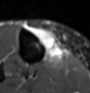
MRI of an extremity soft-tissue mass, one axial slice. Slice 25 of 60 in the series (ordered by position). STIR. MR volume resampled by the dataset authors to the PET/CT grid (not the native acquisition matrix). 3.27 mm slice thickness. 90 × 93 image matrix, field of view 88 × 91 mm. Female patient. Case-level facts recorded for this patient, not image findings: histological type: undifferentiated – high grade; grade: high; site of the primary tumour: right thigh.
Structures marked on this image (expert contour drawn on MRI and transferred to this co-registered scan by the dataset authors):
- gross tumour volume (mass): bounding box <31,26,63,61> (left, top, right, bottom; pixels)